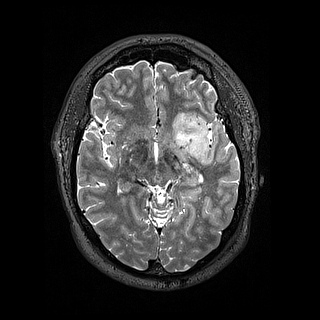
Brain MRI from a brain-tumour surgery series, one axial slice; position 91 of 144 along the scan axis; 320 × 320 image matrix, field of view 254 × 254 mm. Case-level facts recorded for this patient, not image findings: histopathology: Astrocytoma; WHO grade: 2; IDH mutation: yes; tumour location: Left Insular.
Structures marked on this image (expert manual segmentation):
- tumour: bounding box (x1, y1, x2, y2) in pixels: (173, 110, 210, 159)